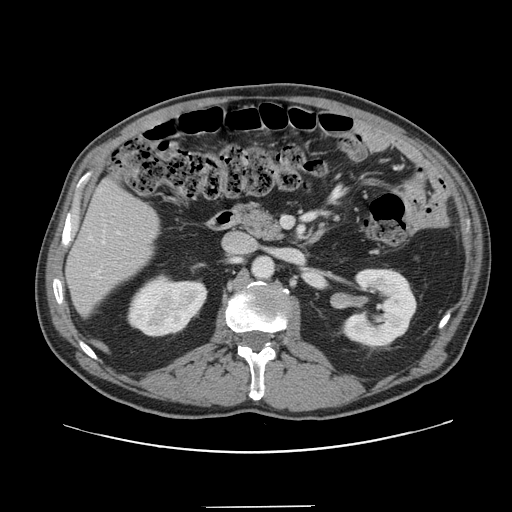
Contrast-enhanced abdominal CT, one axial slice; slice 65 of 139 in the series (ordered by position); intravenous contrast given; soft-tissue window (W 400 / L 40 HU); 2.5 mm slice thickness; 512 × 512 image matrix, field of view 397 × 397 mm. Male patient, age 64 years. Case-level facts recorded for this patient, not image findings: diagnosis: colorectal cancer liver metastases, imaged before liver resection; multiple liver metastases: yes; largest metastasis: 3.5 cm; disease in both lobes: yes.
Structures marked on this image (manually delineated by an expert):
- hepatic veins: box from (x=102, y=241) to (x=105, y=243) px
- liver: (x=67, y=182)–(x=159, y=314)
- planned liver remnant (the part of the liver to remain after resection): (x=68, y=182)–(x=159, y=314)
- portal vein (with intrahepatic branches): (x=117, y=232)–(x=119, y=234)